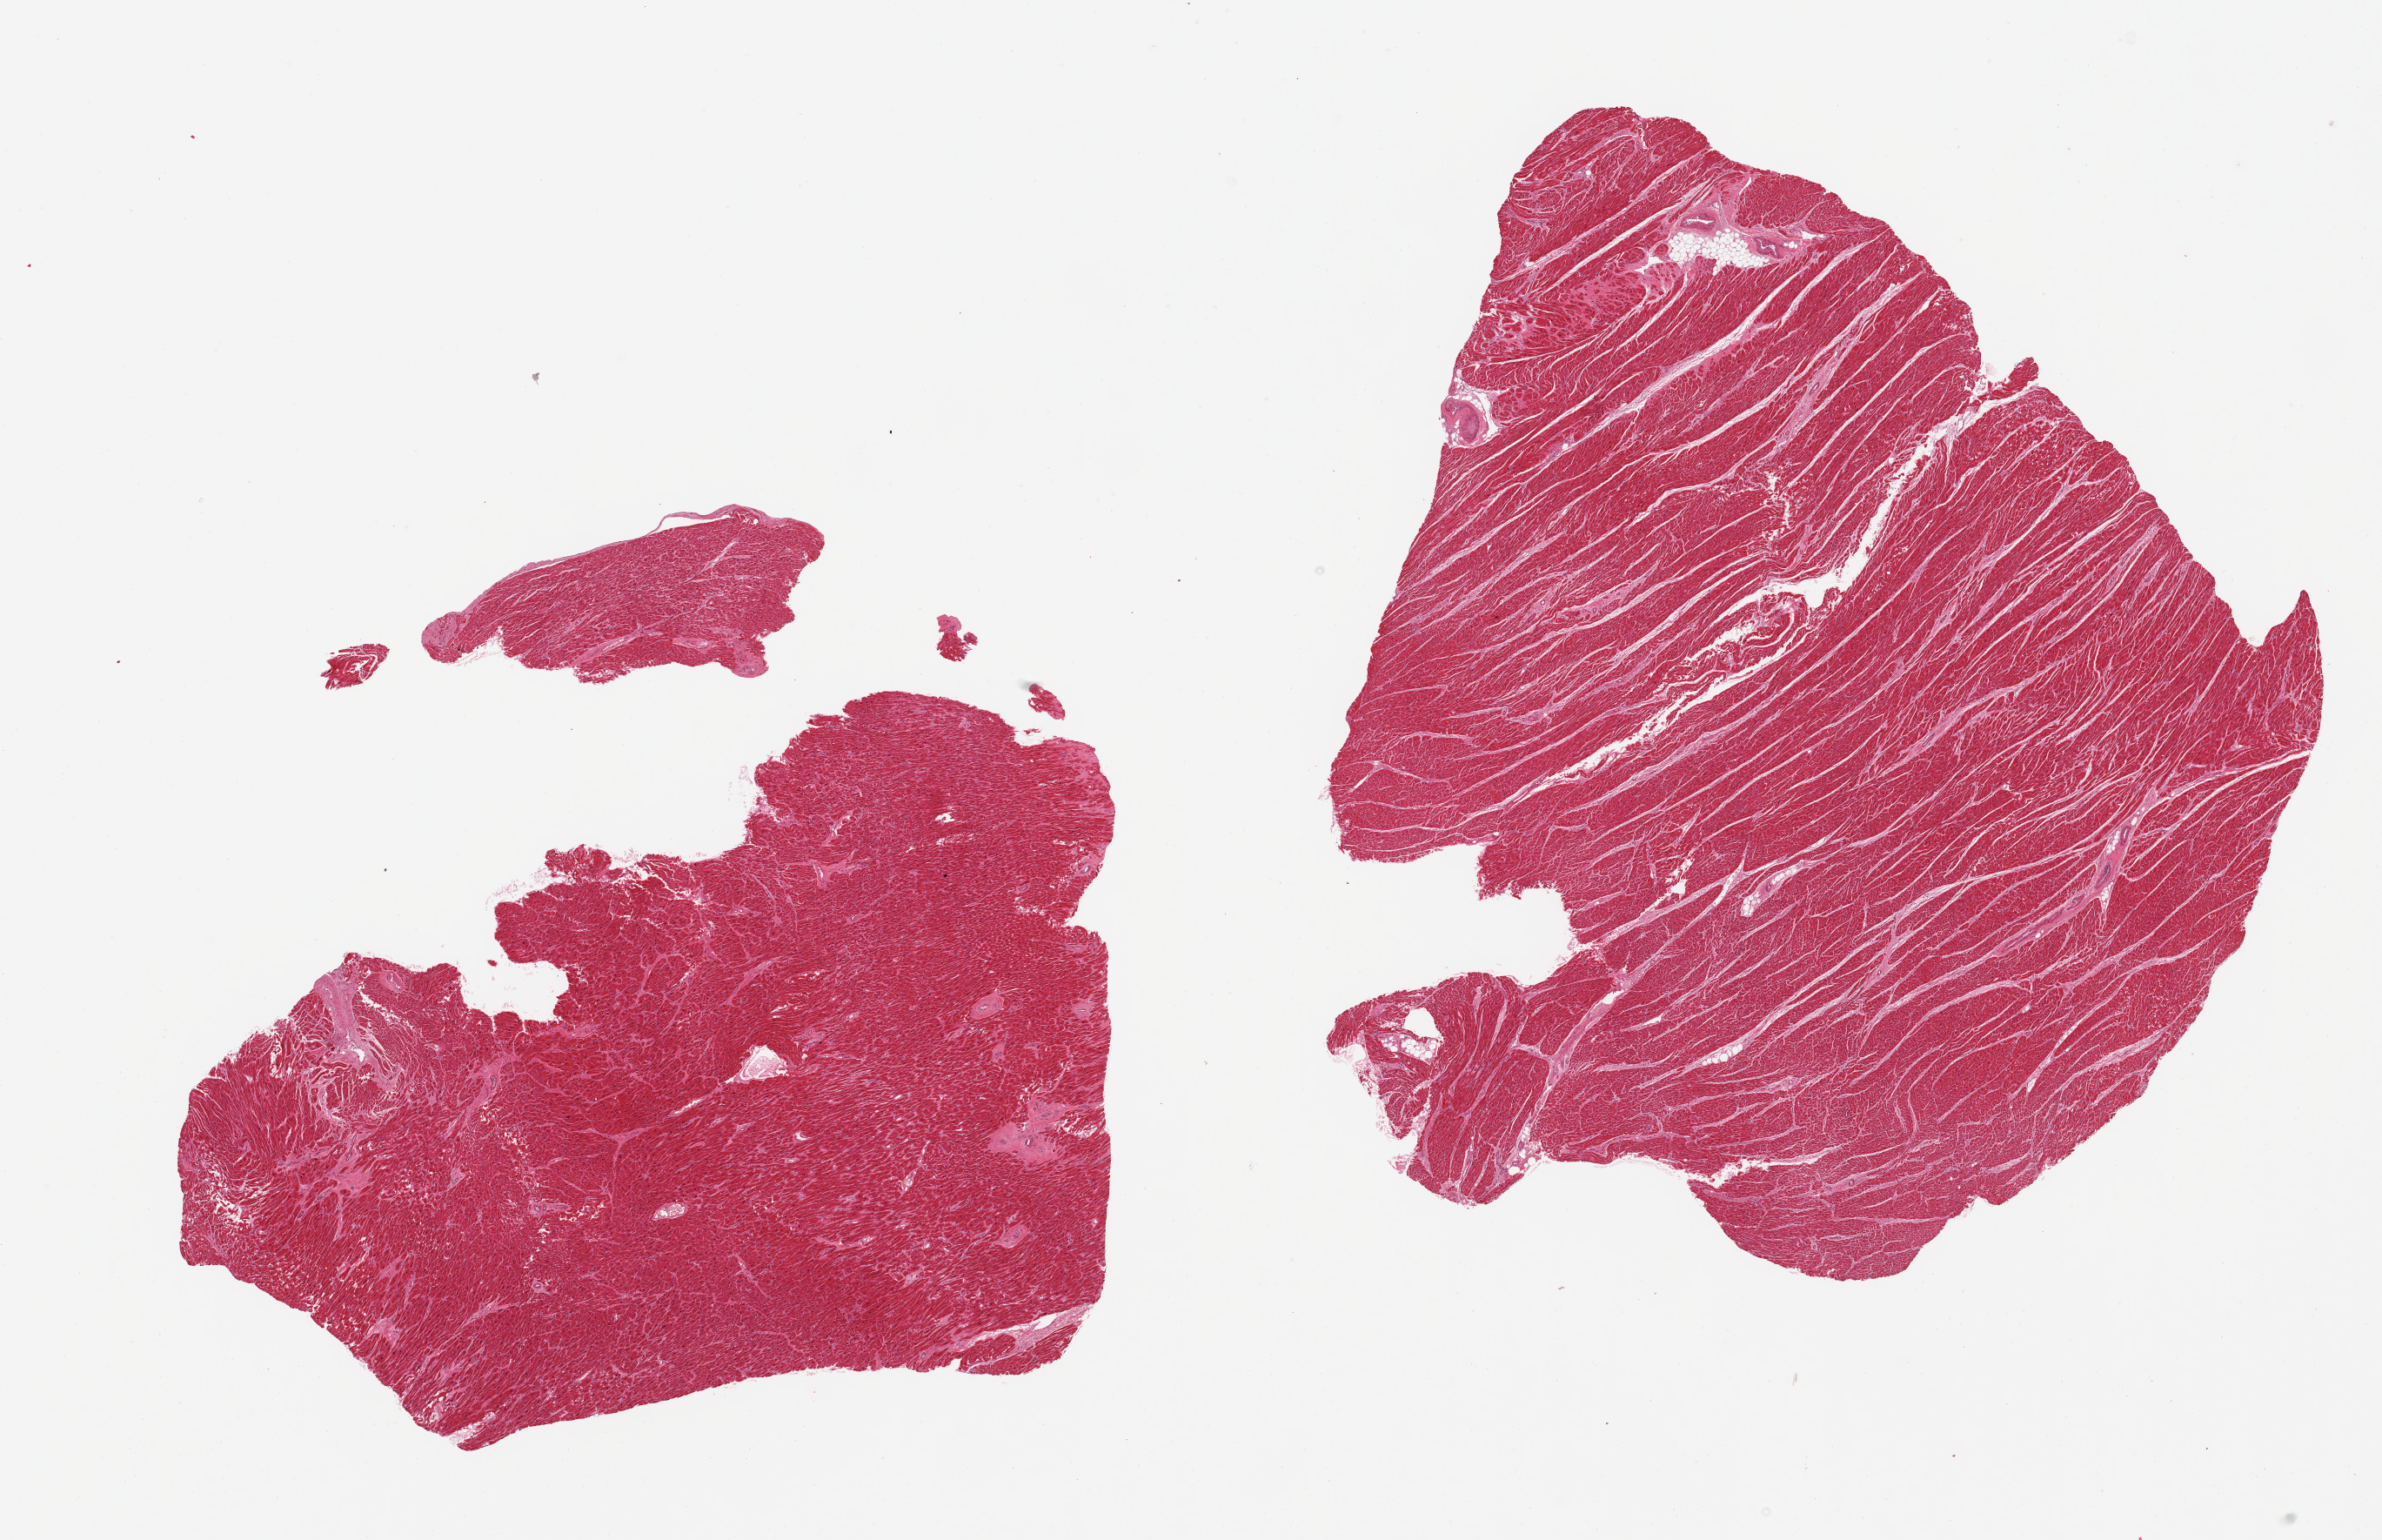
Haematoxylin and eosin whole-slide image — low-resolution overview of the scanned area, about 21.7 x 14.0 mm (acquisition: 20x scan), PAXgene-fixed, paraffin-embedded tissue, target tissue: heart, donor tissue sample. Donor: male.
Review note (as recorded): 2 pieces; interstitial fibrosis with focal scarring.